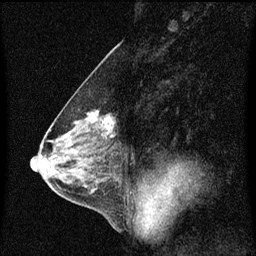
Breast MRI (dynamic contrast-enhanced), one sagittal slice; position 34 of 60 along the scan axis; dynamic contrast-enhanced series, image 2 of 3 at this slice position (ordered by acquisition); 1.5 T; TE 4.2 ms, TR 8.4 ms; 2 mm slice thickness; 256 × 256 image matrix. Patient: female, 58 years.
Structures marked on this image (semi-automatic segmentation, software-assisted and operator-edited):
- analysis volume of interest (the breast-tissue region the enhancement analysis was run in; not a lesion): bounding box (x1, y1, x2, y2) in pixels: (79, 110, 117, 143)
- tumour enhancement mask (voxels above the 70 % enhancement threshold inside the analysis volume of interest): (87, 112, 115, 139)